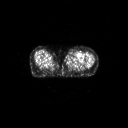
FDG PET of an extremity soft-tissue mass (from a PET/CT study), one axial slice. 3.27 mm slice thickness. 128 × 128 image matrix. Female patient, age 74 years. Case-level facts recorded for this patient, not image findings: histological type: pleomorphic leiomyosarcoma; grade: high; site of the primary tumour: left thigh.
Structures marked on this image (expert contour drawn on MRI and transferred to this co-registered scan by the dataset authors):
- gross tumour volume including surrounding oedema: bounding box [x1, y1, x2, y2] px = [66, 54, 76, 60]